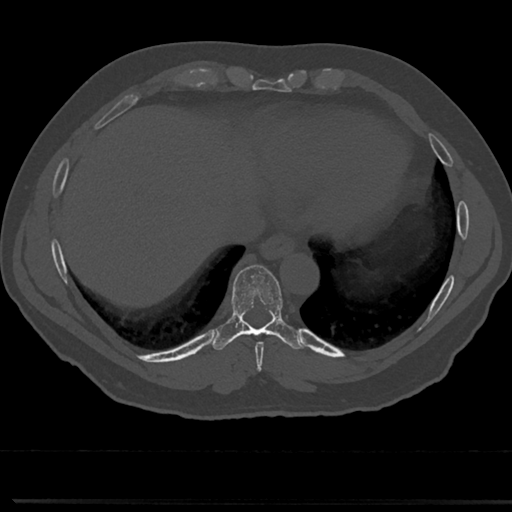
CT including the spine, one axial slice; slice 313 of 817 in the series (ordered by position); 120 kVp; bone window (W 1800 / L 400 HU); 512 × 512 image matrix, field of view 355 × 355 mm. Patient: male, 61 years. From the clinical record (not read from this slice): primary cancer: prostate.
Outlined on this slice (semi-automatic segmentation, software-assisted and operator-edited):
- T7 vertebra: bounding box (x1, y1, x2, y2) in pixels: (261, 365, 264, 368)
- T8 vertebra: (230, 268, 292, 352)
- T9 vertebra: (235, 268, 281, 327)